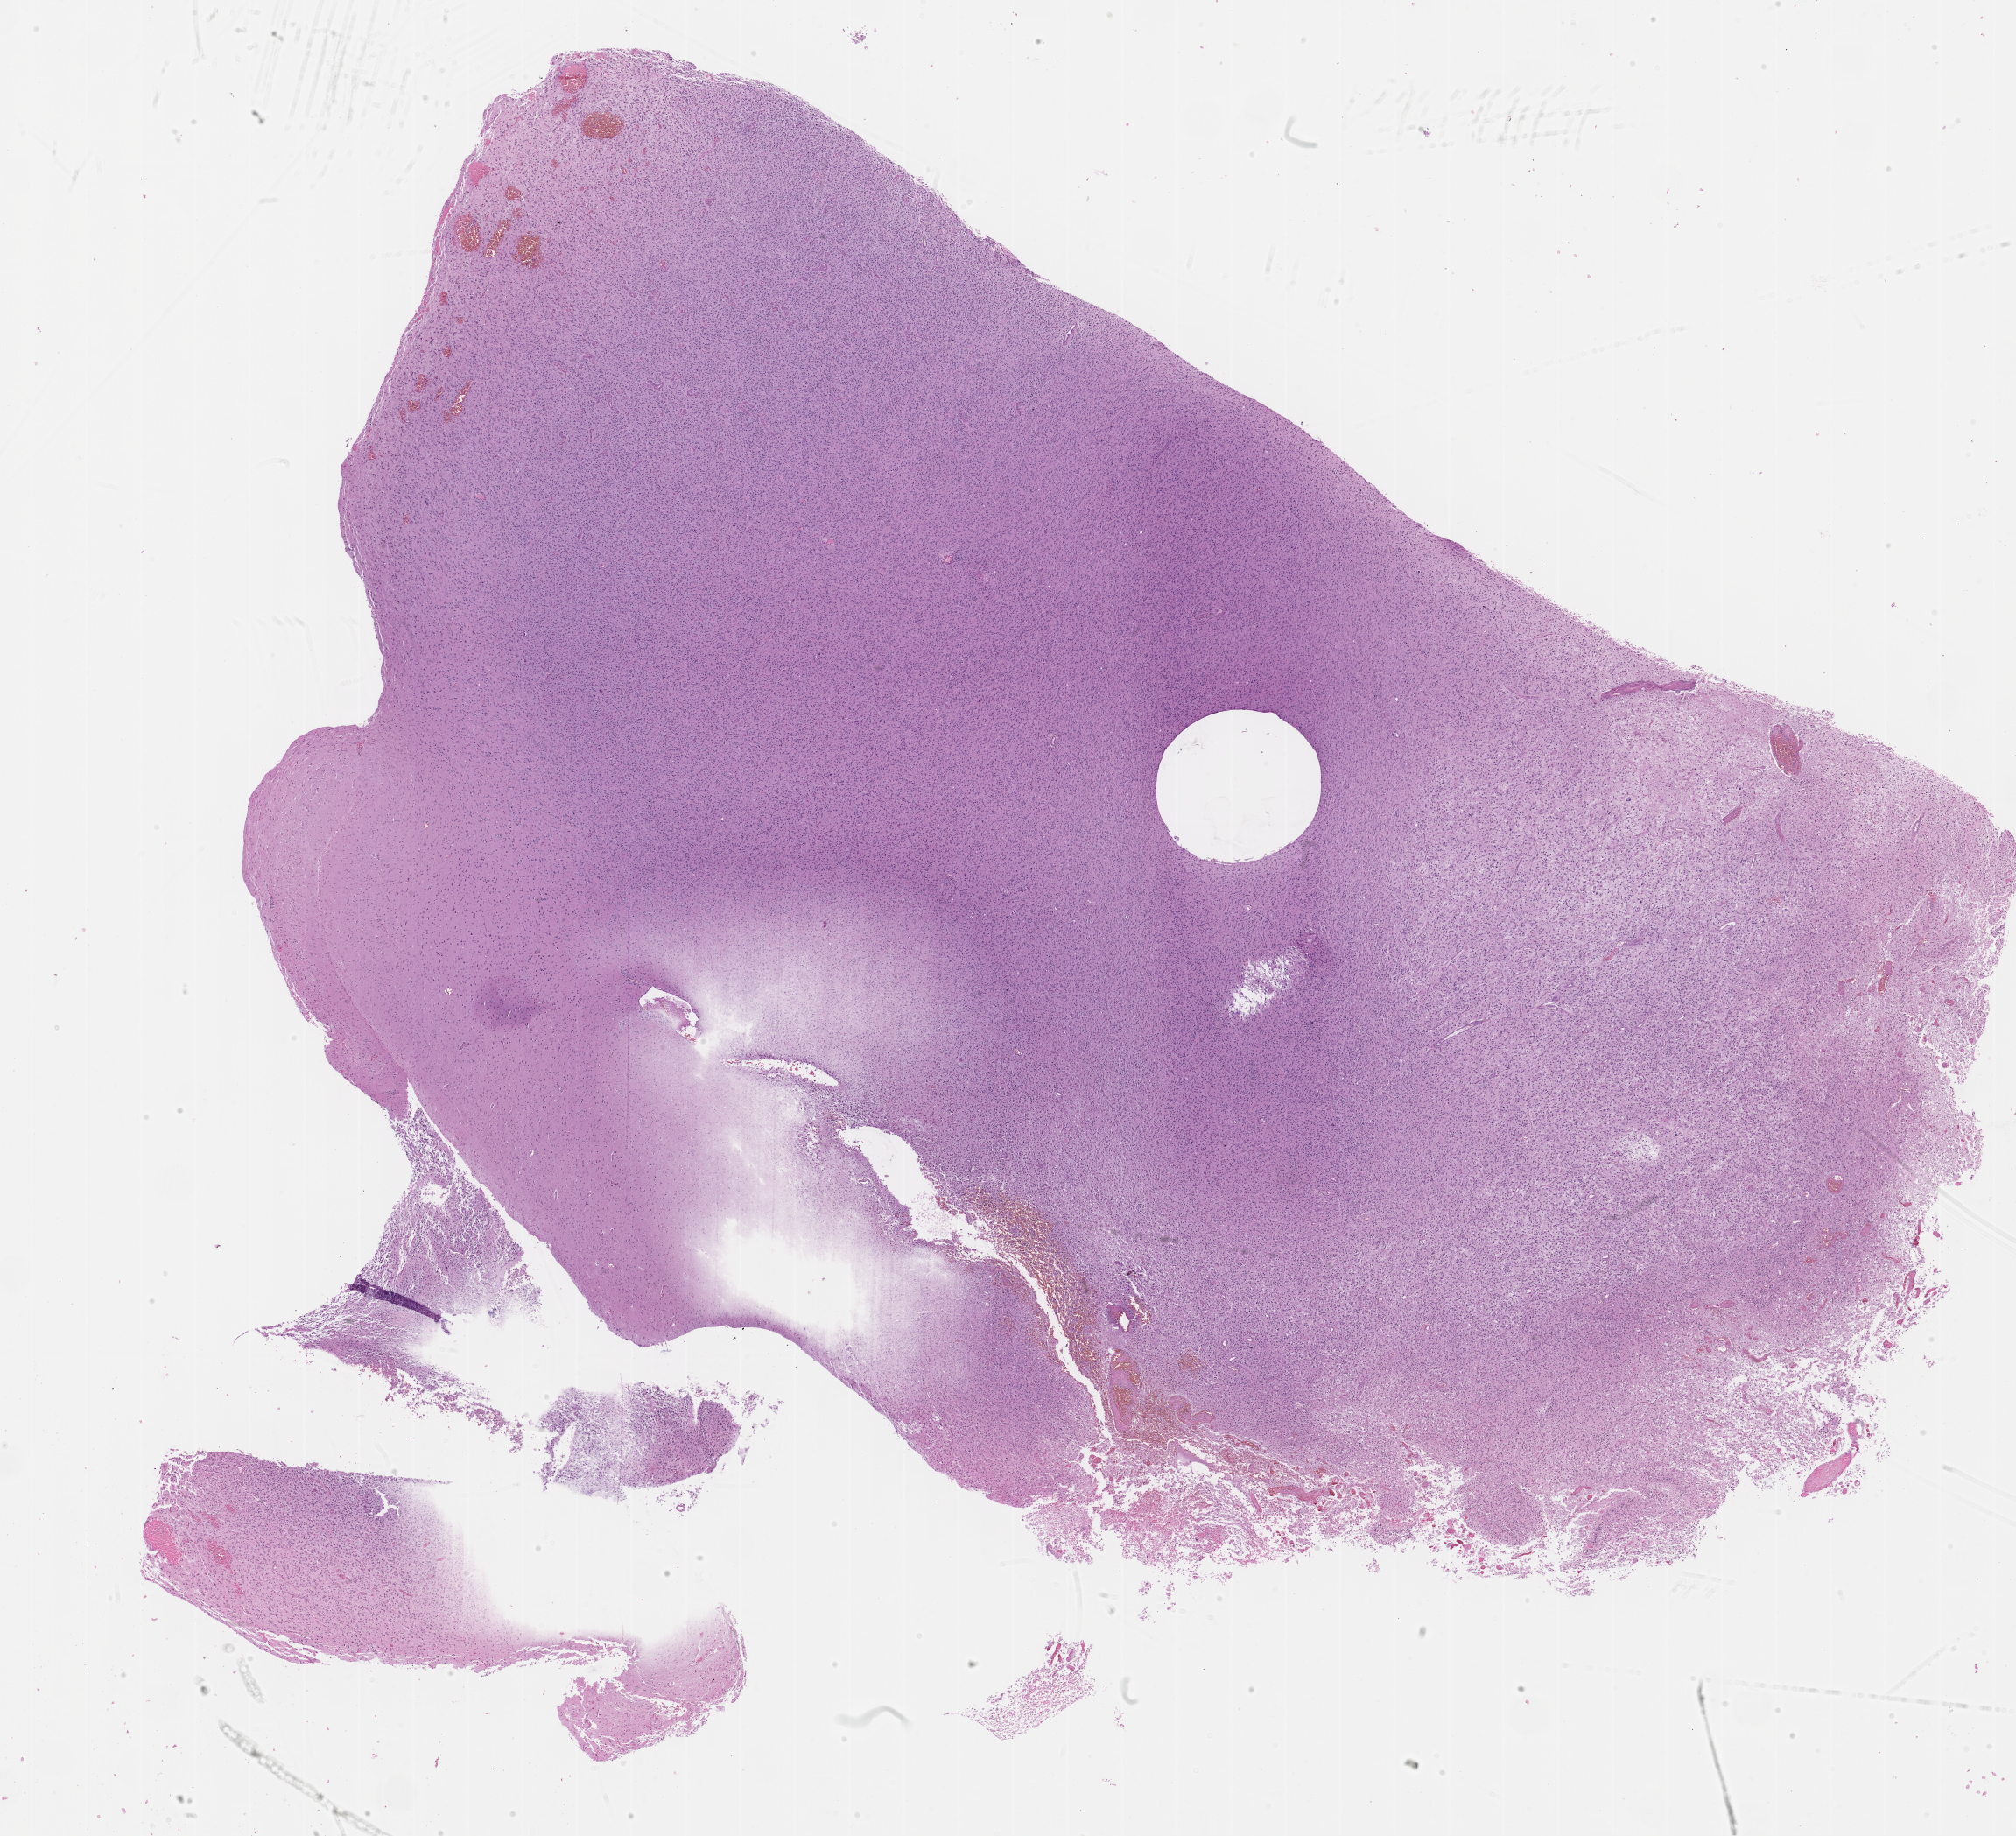
H&E whole-slide image, a low-resolution overview of the entire scanned area, about 18.7 x 17.0 mm. Formalin-fixed paraffin-embedded (FFPE) diagnostic section. Primary tumour sample from the brain. Male patient; age at initial diagnosis 60 years.
* diagnosis: Glioblastoma